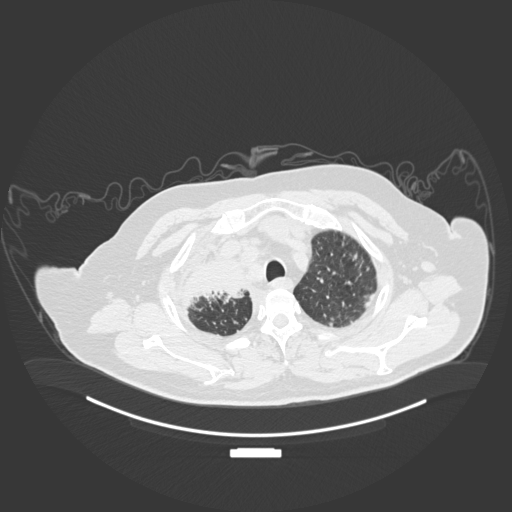
Chest CT, one axial slice; position 159 of 201 along the scan axis; reconstruction kernel B30f; 120 kVp; lung window (W 1500 / L -600 HU); 512 × 512 image matrix, field of view 500 × 500 mm. Patient: male, 69 years. Case-level facts recorded for this patient, not image findings: clinical TNM (as recorded): T4 N3 M1.
Structures marked on this image (rectangle marked by the reading radiologist):
- lung tumour (recorded histology: adenocarcinoma): bounding box (x1, y1, x2, y2) in pixels: (180, 258, 267, 314)